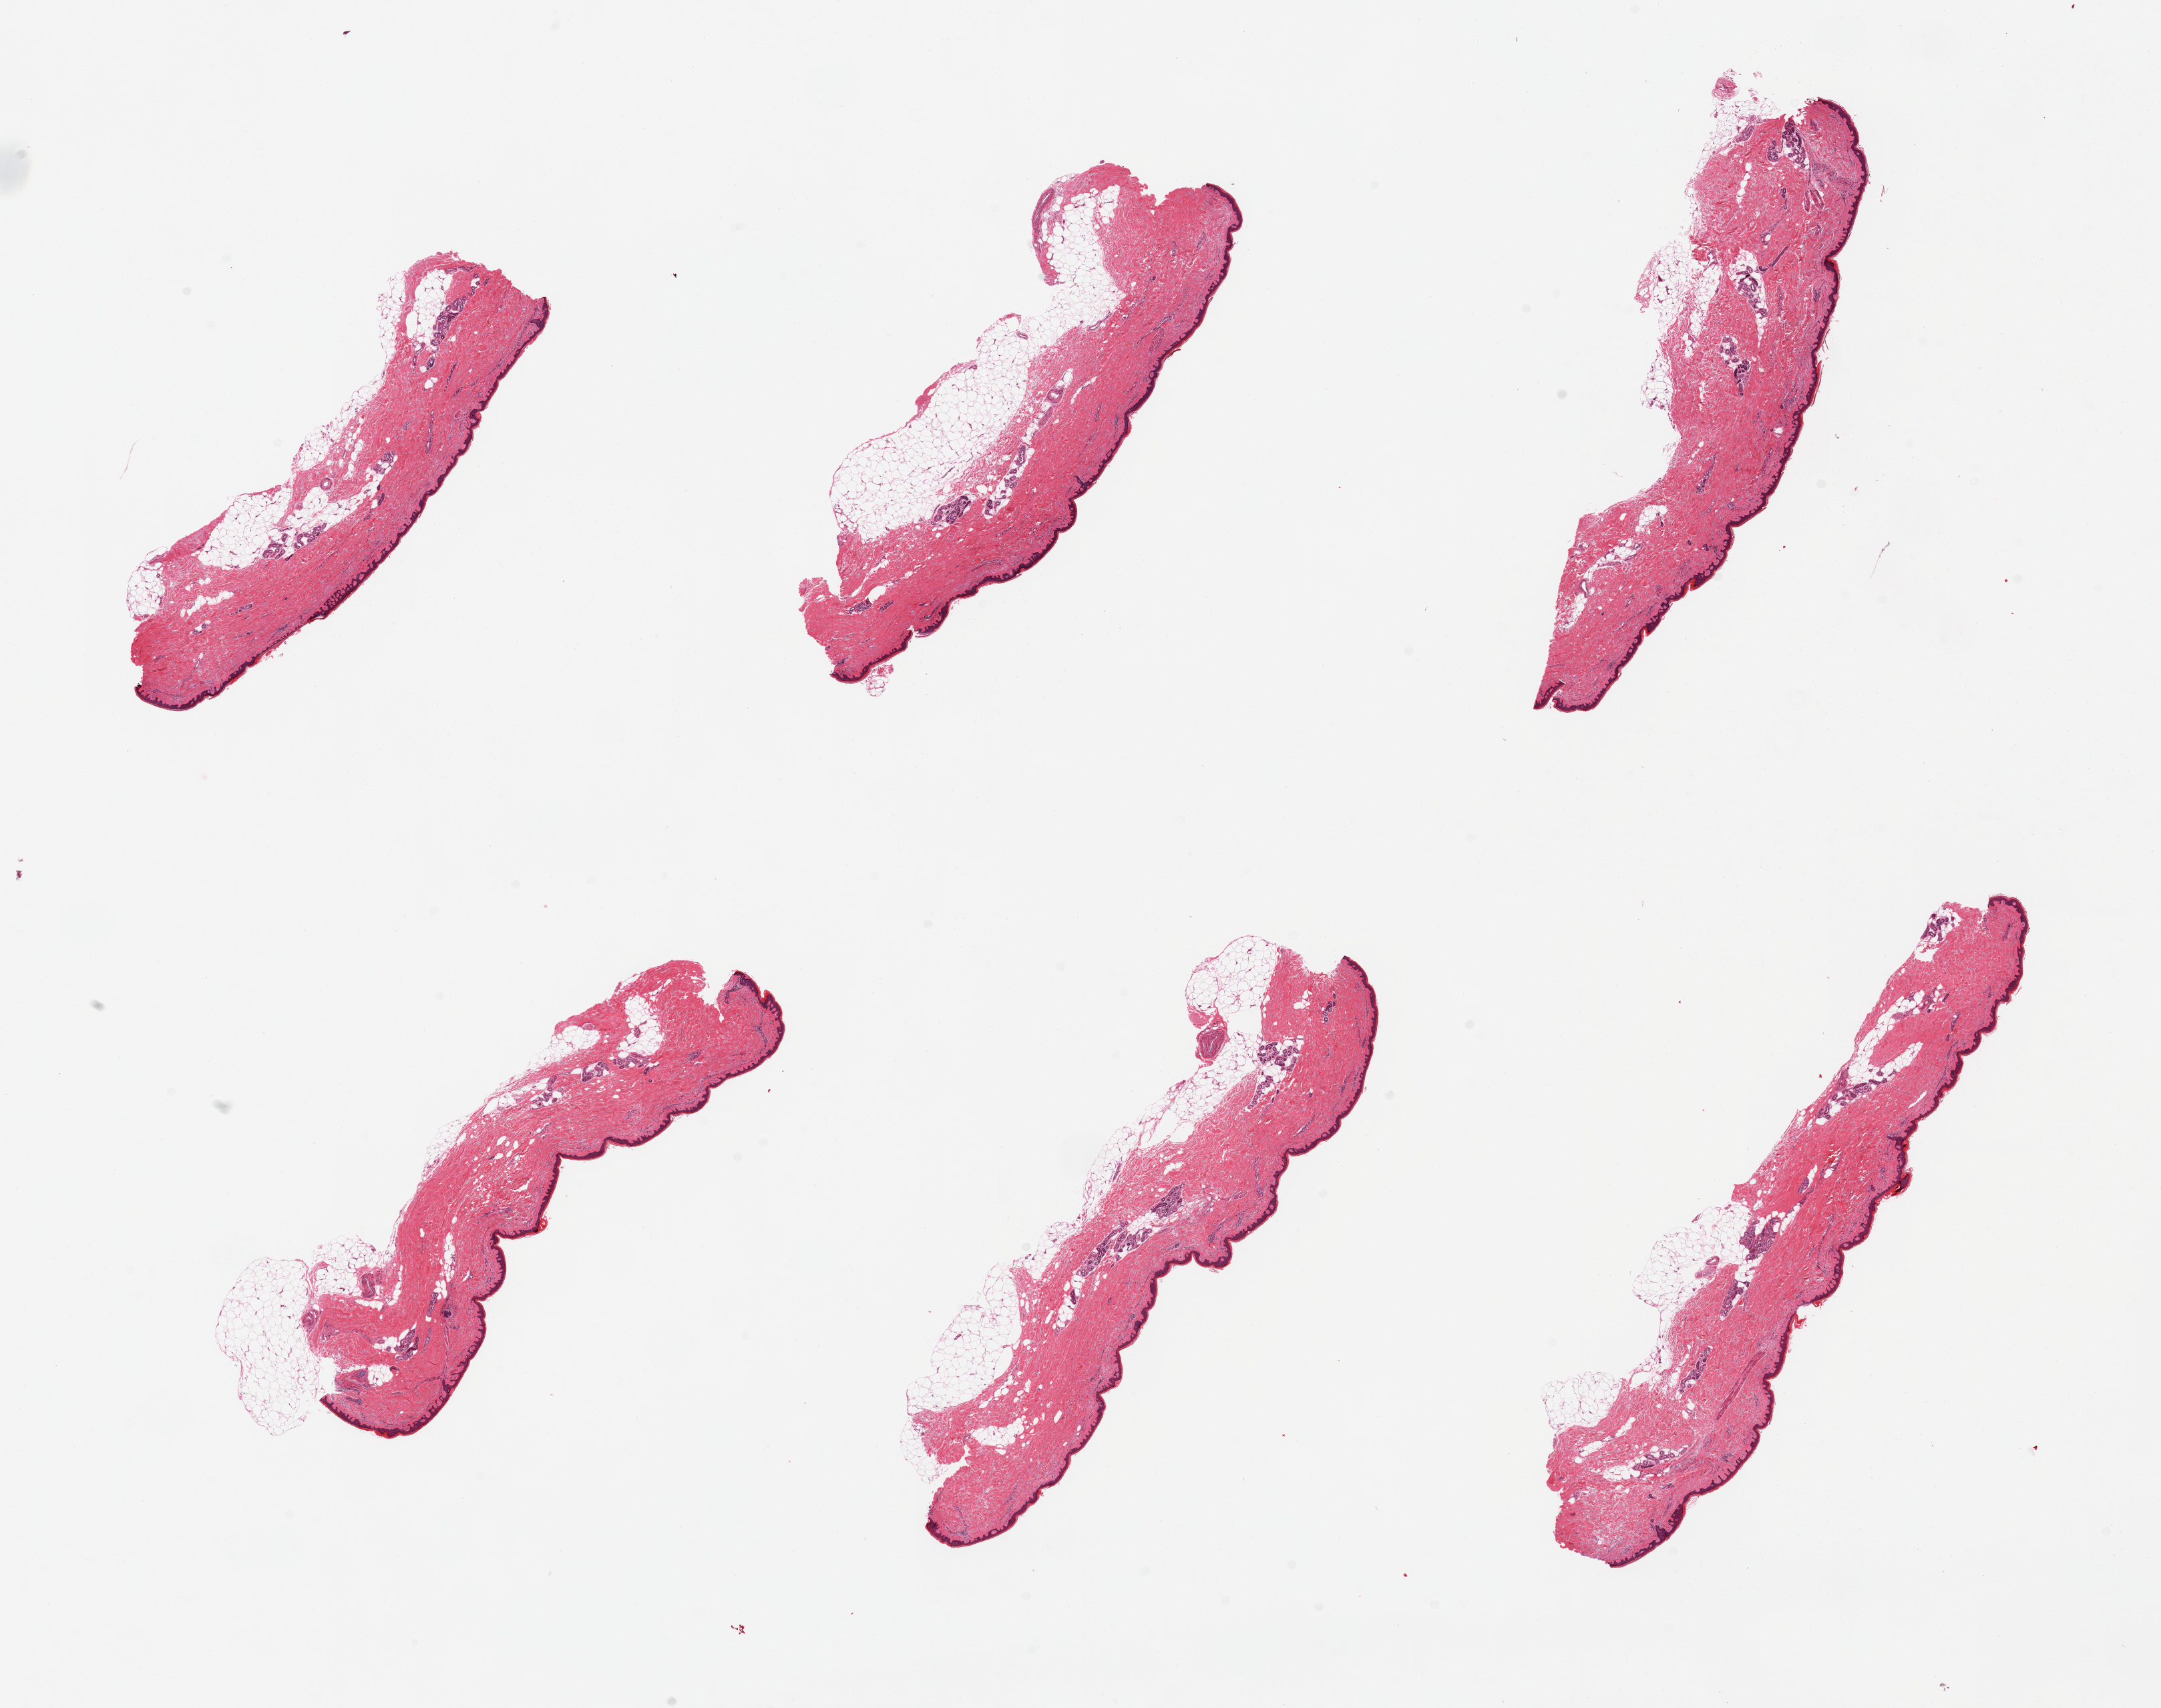
Digitized hematoxylin and eosin (H&E)-stained section — shown as a low-resolution overview of the whole scanned area (about 25.6 x 20.2 mm, acquisition: 20x scan), PAXgene-fixed, paraffin-embedded tissue, section of skin of lower leg (target tissue), donor tissue sample.
- pathologist's review note for this sample: 6 pieces; up to 1 mm subcutaneous fat on all pieces